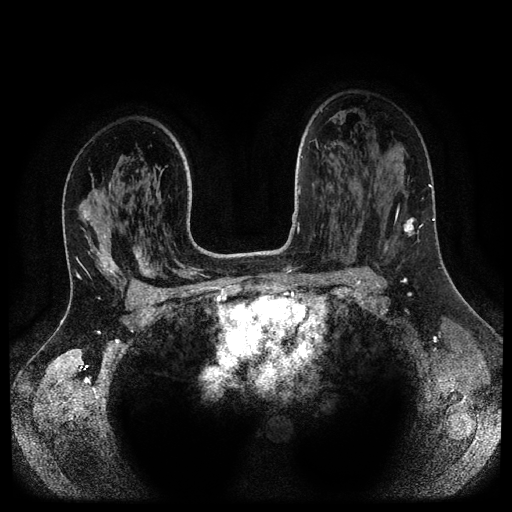
Breast MRI (dynamic contrast-enhanced, multi-phase), one axial slice. Slice 70 of 116 in the series (ordered by position). Dynamic contrast-enhanced series, time point 2 of 5 at this slice position (early post-contrast). 1.5 T. TE 2.6 ms, TR 5.3 ms. 2.1 mm slice thickness. 512 × 512 image matrix, field of view 360 × 360 mm. Female patient, age 37 years.
Outlined on this slice (semi-automatic segmentation, software-assisted and operator-edited):
- breast lesion (labelled 'tumour' in the annotation; benign lesions carry a separate 'benign' label): bounding box (x1, y1, x2, y2) in pixels: (403, 217, 416, 237)